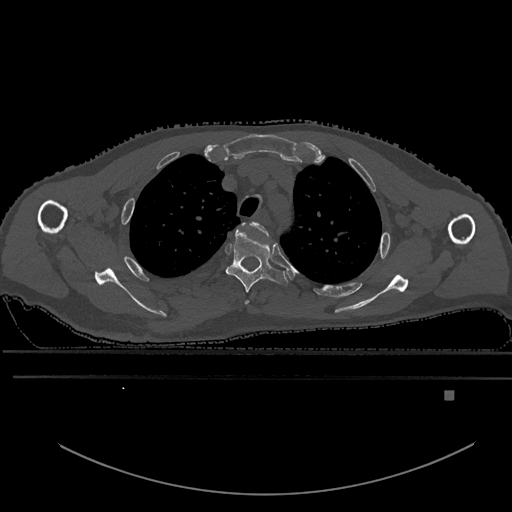
CT including the spine, one axial slice; slice 455 of 969 in the series (ordered by position); bone window (W 1800 / L 400 HU); 512 × 512 image matrix, field of view 456 × 456 mm. Male patient, age 82 years. Case-level facts recorded for this patient, not image findings: primary cancer: prostate; vertebrae with lytic lesions (as recorded): T11, T9, T8, T2.
Structures marked on this image (semi-automatic segmentation, software-assisted and operator-edited):
- T2 vertebra: bounding box <241,222,268,304> (left, top, right, bottom; pixels)
- T3 vertebra: <226,231,289,293>